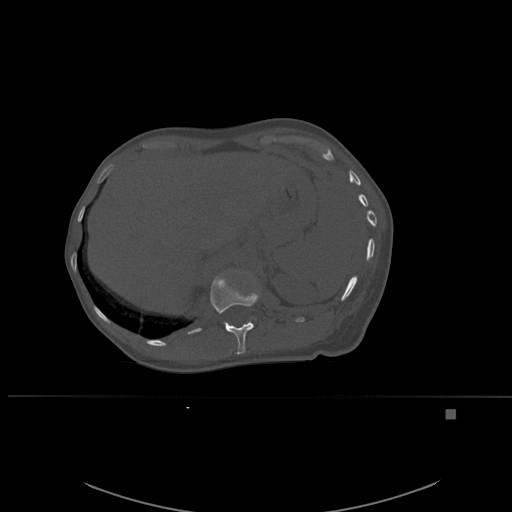
CT including the spine, one axial slice. Slice 275 of 537 in the series (ordered by position). Bone window (W 1800 / L 400 HU). 1.5 mm slice thickness. 512 × 512 image matrix, field of view 440 × 440 mm. Female patient, age 45 years. From the clinical record (not read from this slice): primary cancer: lung.
Annotated regions visible in this slice (semi-automatic segmentation, software-assisted and operator-edited):
- T12 vertebra: box from (x=210, y=271) to (x=260, y=355) px